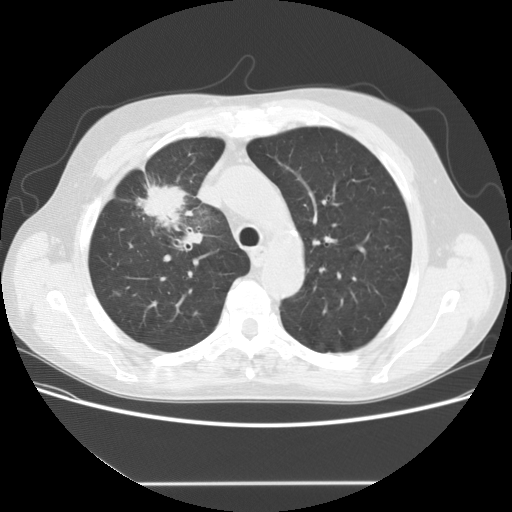
Low-dose screening chest CT, one axial slice; position 113 of 153 along the scan axis; reconstruction kernel STANDARD; 120 kVp; lung window (W 1500 / L -600 HU); 2.5 mm slice thickness; 512 × 512 image matrix, field of view 360 × 360 mm.
Structures marked on this image (manually delineated by an expert):
- lesion 1 (tumor, upper lobe of right lung): bounding box (x1, y1, x2, y2) in pixels: (136, 183, 193, 231)